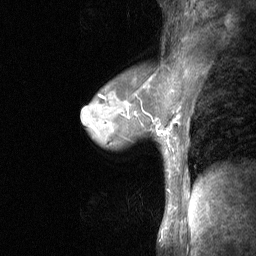
Breast MRI (dynamic contrast-enhanced), one sagittal slice; position 41 of 64 along the scan axis; dynamic contrast-enhanced study with each time point stored as its own series, time point 2 of 3 at this slice position (early post-contrast, ordered by acquisition time); 1.5 T; TE 4.8 ms, TR 27 ms; 2 mm slice thickness; 256 × 256 image matrix, field of view 200 × 200 mm. Female patient, age 44 years. From the clinical record (not read from this slice): setting: breast cancer imaged before/during neoadjuvant chemotherapy; receptor status: HR-positive, HER2-negative.
Annotated regions visible in this slice (semi-automatically segmented with operator editing):
- analysis volume of interest (the breast-tissue region the enhancement analysis was run in; not a lesion): bounding box <140,109,180,148> (left, top, right, bottom; pixels)
- tumour enhancement mask (voxels above the 90 % enhancement threshold inside the analysis volume of interest): <143,111,179,134>